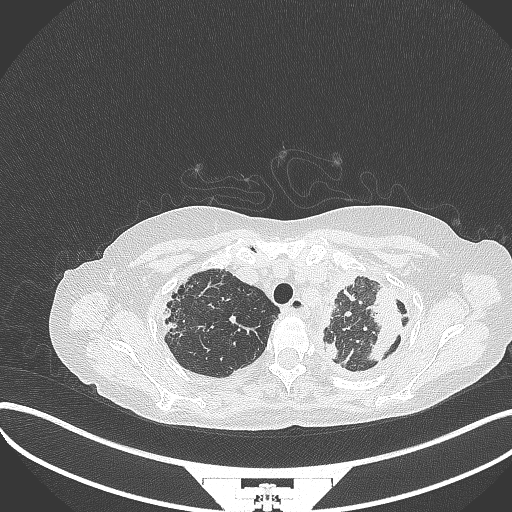
Chest CT, one axial slice. Position 283 of 373 along the scan axis. Reconstruction kernel B70f. Lung window (W 1500 / L -600 HU). 1 mm slice thickness. 512 × 512 image matrix. Female patient, age 56 years. Case-level facts recorded for this patient, not image findings: clinical TNM (as recorded): T1 N0 M0.
Structures marked on this image (rectangle marked by the reading radiologist):
- lung tumour (recorded histology: adenocarcinoma): bounding box (x1, y1, x2, y2) in pixels: (365, 277, 407, 365)